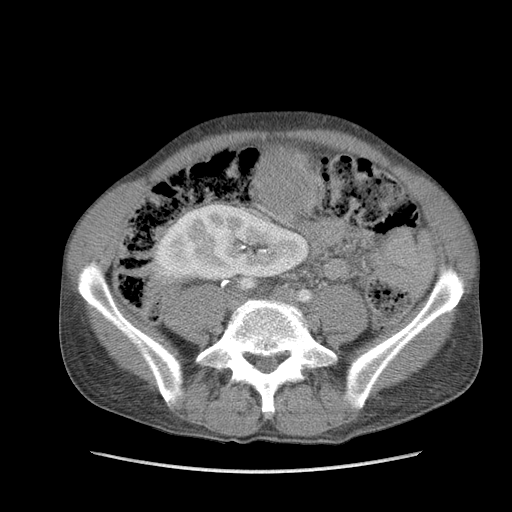
Contrast-enhanced abdominal CT, one axial slice. Position 36 of 115 along the scan axis. Soft-tissue window (W 400 / L 40 HU). 5 mm slice thickness. 512 × 512 image matrix, field of view 360 × 360 mm. Male patient. From the clinical record (not read from this slice): diagnosis: adrenocortical carcinoma; tumour side: right adrenal; Ki-67 index: 13 %; stage (as recorded): 3.
Outlined on this slice (semi-automatically segmented with operator editing):
- mass: bounding box (x1, y1, x2, y2) in pixels: (253, 144, 319, 218)